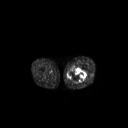
FDG PET of an extremity soft-tissue mass (from a PET/CT study), one axial slice. 3.27 mm slice thickness. 128 × 128 image matrix, field of view 700 × 700 mm. Patient: male, 44 years. From the clinical record (not read from this slice): histological type: undifferentiated pleomorphic liposarcoma; grade: high; site of the primary tumour: left thigh.
Annotated regions visible in this slice (expert contour drawn on MRI and transferred to this co-registered scan by the dataset authors):
- gross tumour volume including surrounding oedema: bounding box [x1, y1, x2, y2] px = [67, 68, 86, 83]
- gross tumour volume (mass): [67, 68, 86, 82]